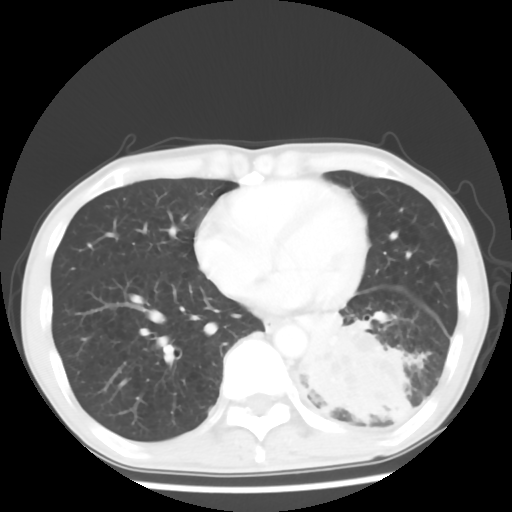
Chest CT, one axial slice; position 22 of 64 along the scan axis; reconstruction kernel STANDARD; lung window (W 1500 / L -600 HU); 5 mm slice thickness; 512 × 512 image matrix. Patient: male, 68 years. From the clinical record (not read from this slice): clinical TNM (as recorded): T4 N0 M0.
Structures marked on this image (rectangle marked by the reading radiologist):
- lung tumour (recorded histology: squamous cell carcinoma): box from (x=294, y=308) to (x=410, y=436) px